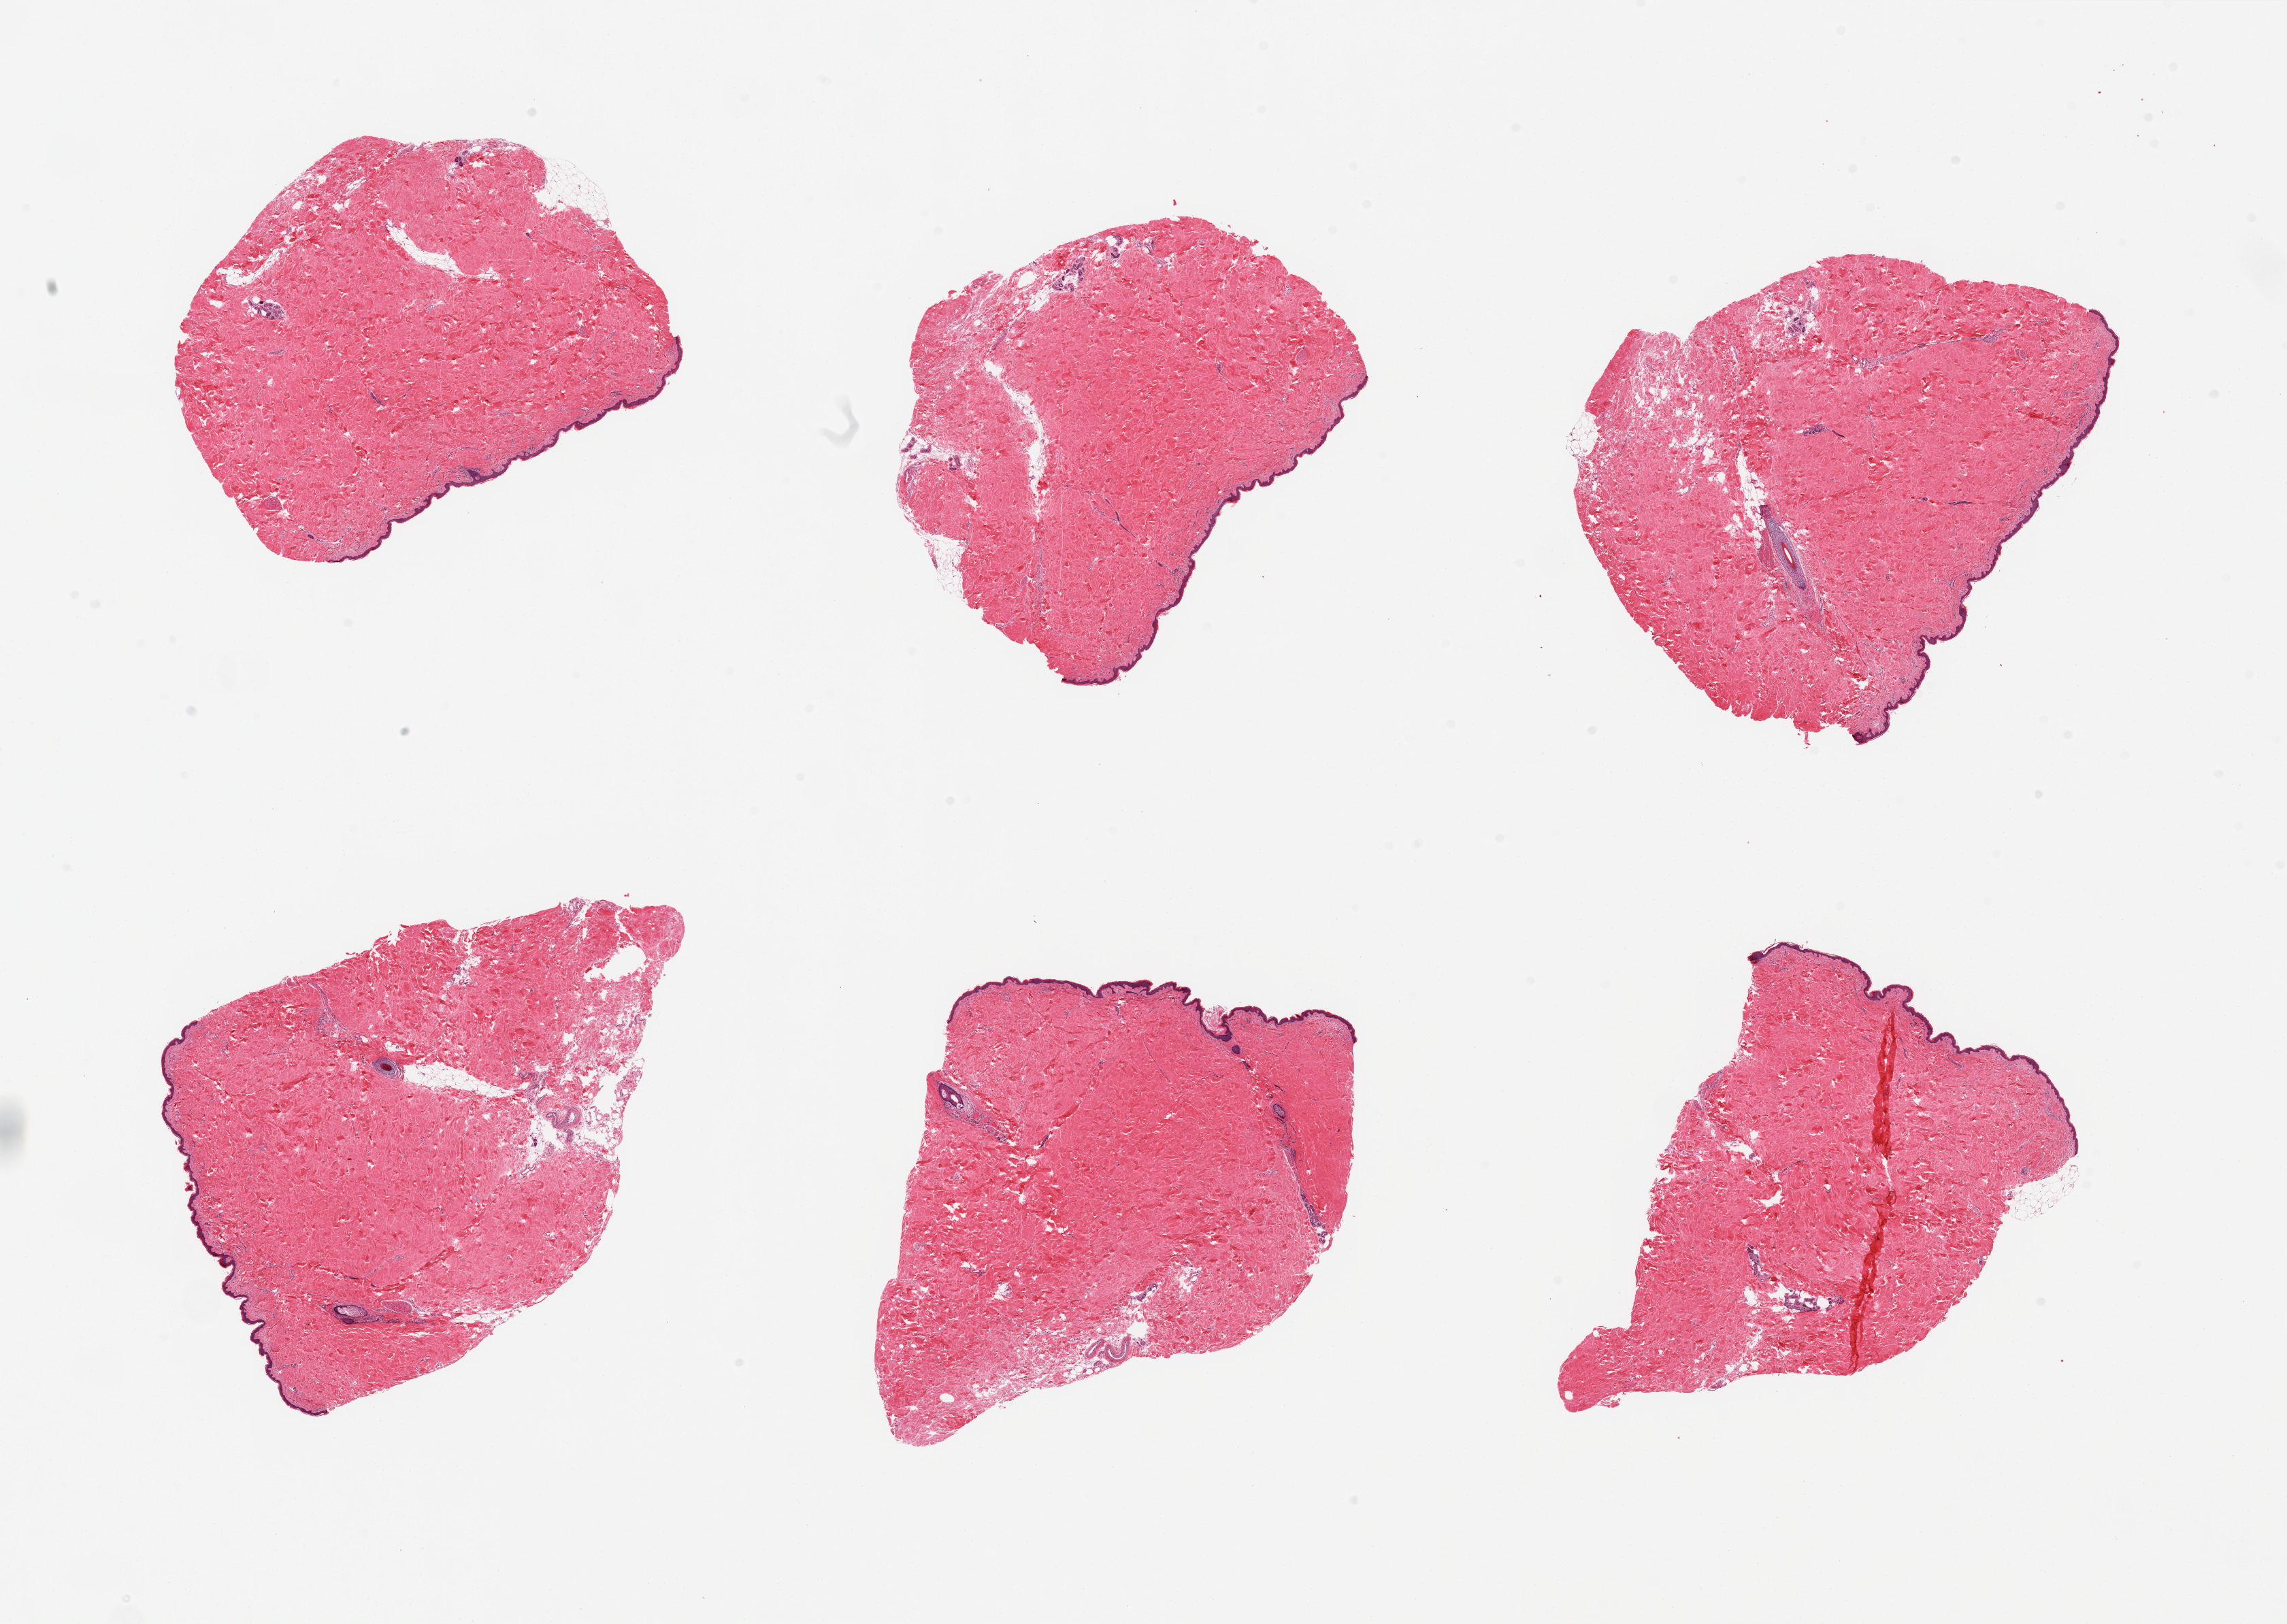
Digitized hematoxylin and eosin (H&E)-stained section, low-resolution overview of the scanned area, about 26.6 x 18.9 mm, PAXgene-fixed, paraffin-embedded tissue, target tissue: skin of suprapubic region, donor tissue sample. Donor: male.
Pathologist's review note for this sample: 6 pieces, no dermal fat; squamous epithelium is ~50 microns.